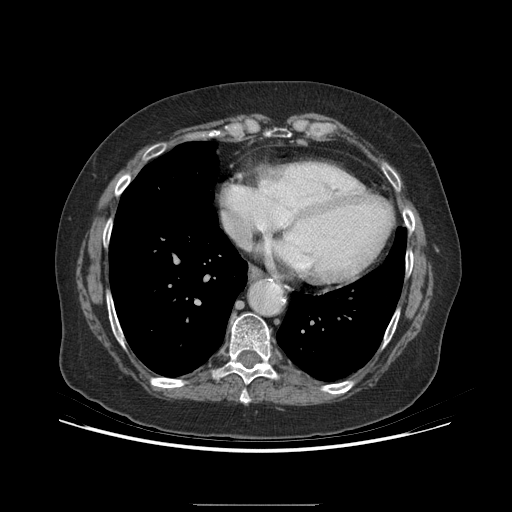
Contrast-enhanced abdominal CT (liver protocol), one axial slice. Slice 191 of 192 in the series (ordered by position). Reconstruction kernel STANDARD. 140 kVp. Soft-tissue window (W 400 / L 40 HU). 2.5 mm slice thickness. 512 × 512 image matrix, field of view 400 × 400 mm. Case-level facts recorded for this patient, not image findings: diagnosis: hepatocellular carcinoma (patient treated with transarterial chemoembolisation; whether this scan precedes or follows treatment is not stated here); TNM stage (as recorded): Stage-I; Child-Pugh class: A.
Annotated regions visible in this slice (semi-automatically segmented with operator editing):
- abdominal aorta: bounding box (x1, y1, x2, y2) in pixels: (250, 282, 281, 314)